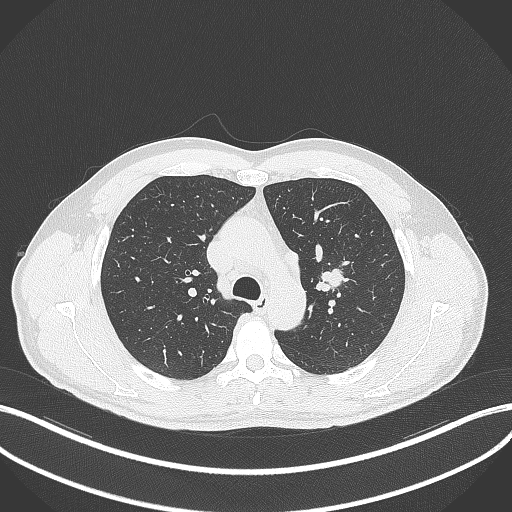
Chest CT, one axial slice. Position 298 of 392 along the scan axis. Reconstruction kernel B70f. 120 kVp. Lung window (W 1500 / L -600 HU). 512 × 512 image matrix, field of view 400 × 400 mm. Male patient, age 50 years. From the clinical record (not read from this slice): clinical TNM (as recorded): T1c N1 M1b.
Annotated regions visible in this slice (rectangle marked by the reading radiologist):
- lung tumour (recorded histology: squamous cell carcinoma): box from (x=313, y=265) to (x=348, y=295) px